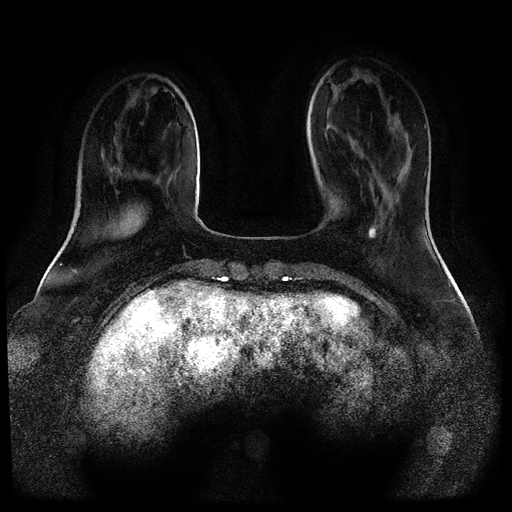
Breast MRI (dynamic contrast-enhanced, multi-phase), one axial slice; position 27 of 116 along the scan axis; dynamic contrast-enhanced series, time point 2 of 5 at this slice position (early post-contrast); 1.5 T; TE 2.6 ms, TR 5.3 ms; 2 mm slice thickness; 512 × 512 image matrix, field of view 360 × 360 mm. Patient: female, 52 years.
Outlined on this slice (semi-automatic segmentation, software-assisted and operator-edited):
- breast lesion (labelled 'tumour' in the annotation; benign lesions carry a separate 'benign' label): box from (x=369, y=227) to (x=377, y=238) px